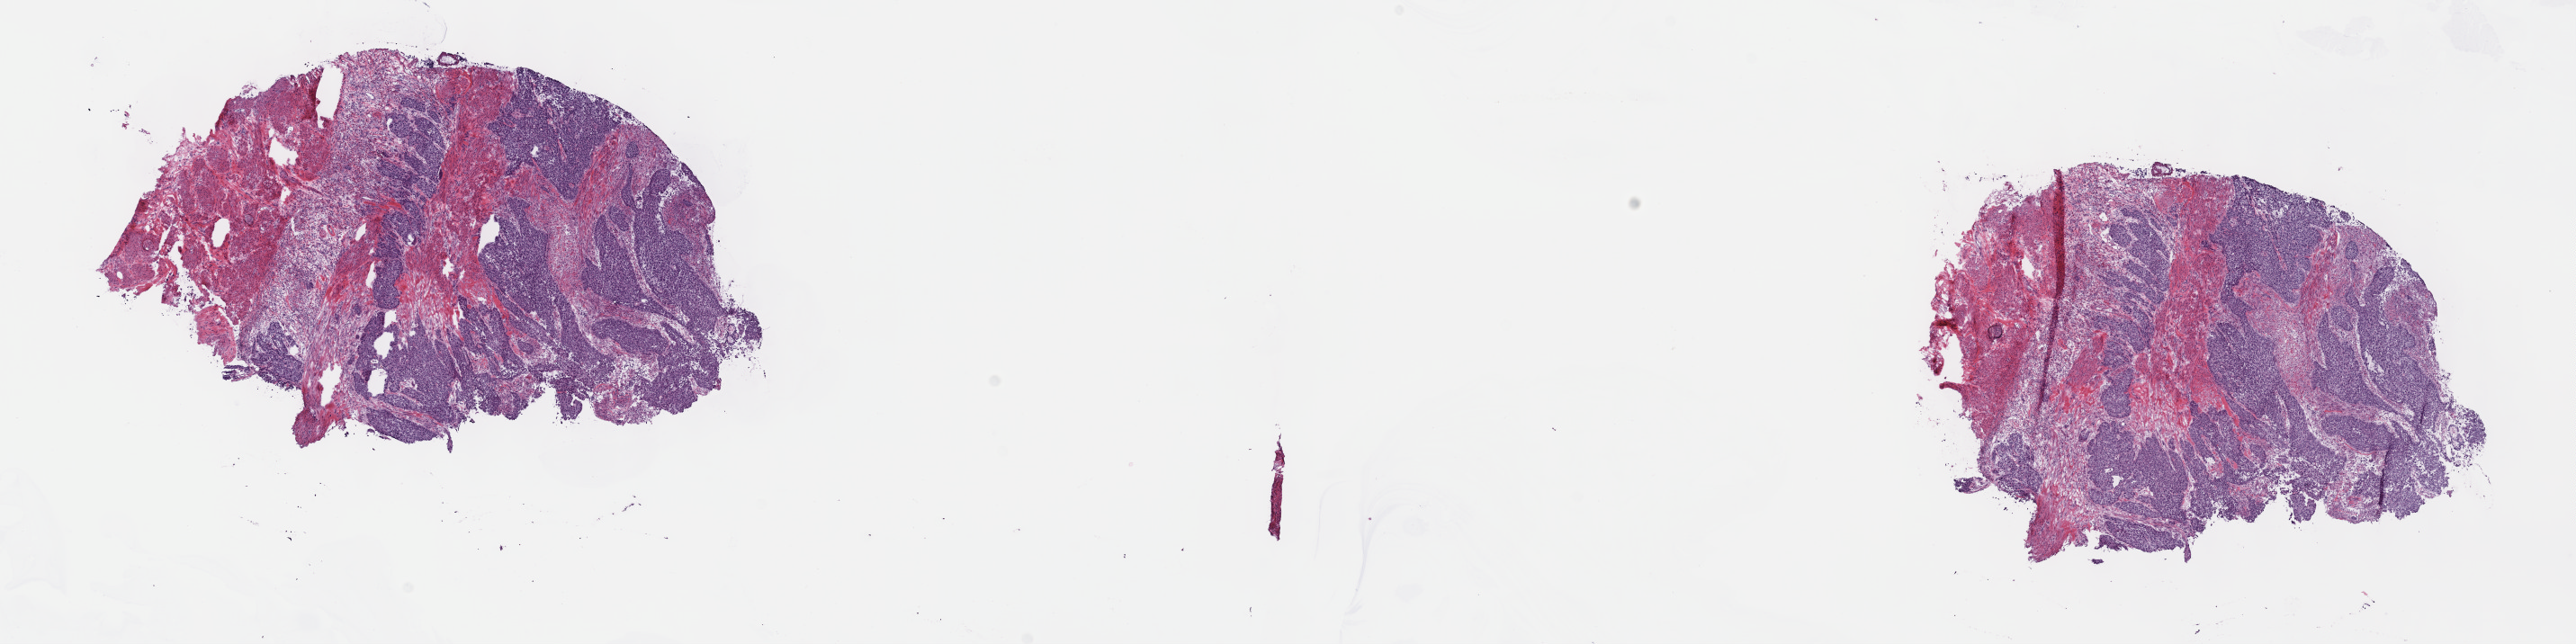
Hematoxylin and eosin (H&E) stained whole-slide image, shown as a low-resolution overview of the whole scanned area (about 23.2 x 5.8 mm, from a 40x scan); frozen section from the top of the tissue portion; sample: primary tumour, bladder. Male, age 57 years at initial diagnosis. Histologic grade: high grade. Pathologist review of this section (percent, as recorded): tumour cells 75%, tumour nuclei 75%, normal cells 0%, stromal cells 25%, necrosis 0%. Inflammatory infiltration, as recorded: lymphocyte infiltration 3%, monocyte infiltration 1%, neutrophil infiltration 5%.
AJCC pathologic stage: II (7th edition). Diagnosis: Transitional cell carcinoma (lateral wall of bladder).